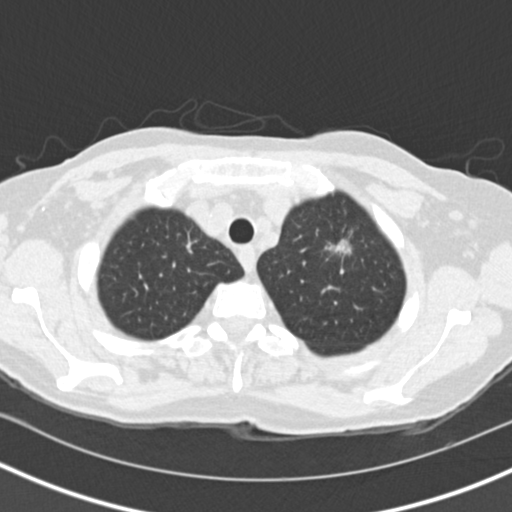
Low-dose screening chest CT, one axial slice; slice 124 of 146 in the series (ordered by position); lung window (W 1500 / L -600 HU); 2 mm slice thickness; 512 × 512 image matrix, field of view 310 × 310 mm.
Annotated regions visible in this slice (expert manual segmentation):
- lesion 1 (tumor, upper lobe of left lung): box from (x=326, y=240) to (x=351, y=254) px